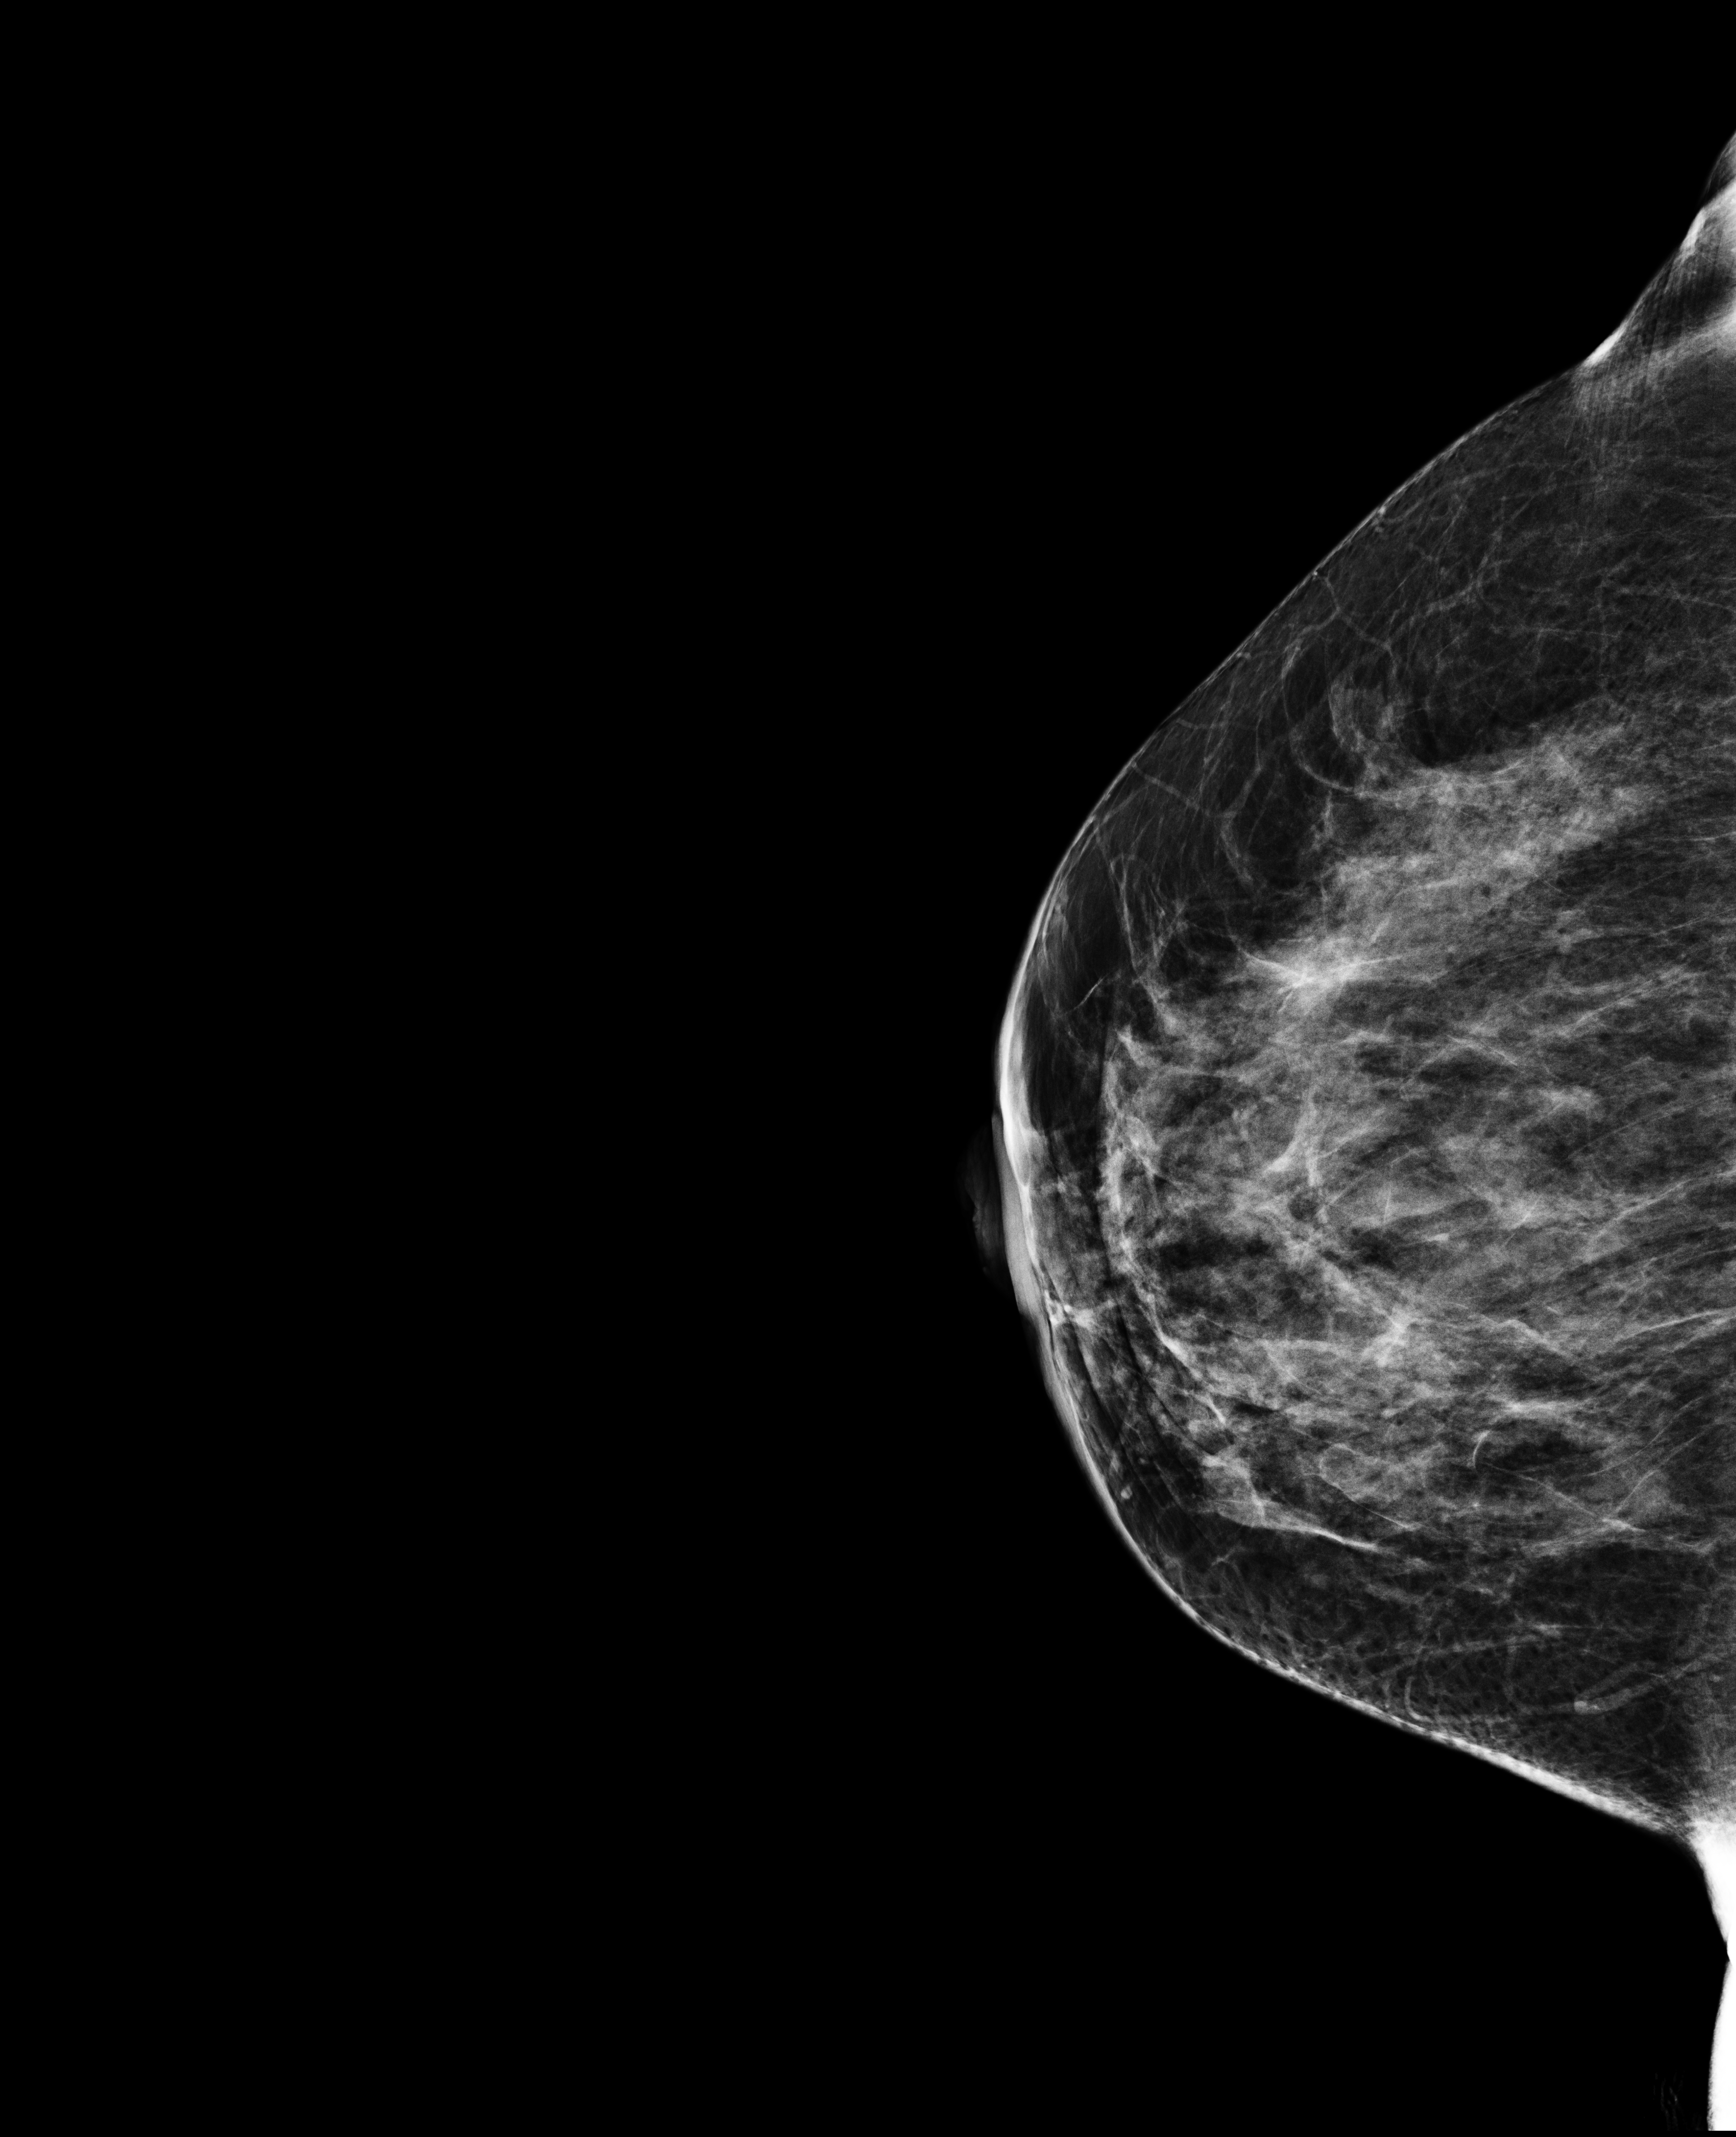
Annual screening mammography examination. Patient: female, 43 years.
Image type: full-field digital mammogram. Breast: right. Projection: cranio-caudal projection.